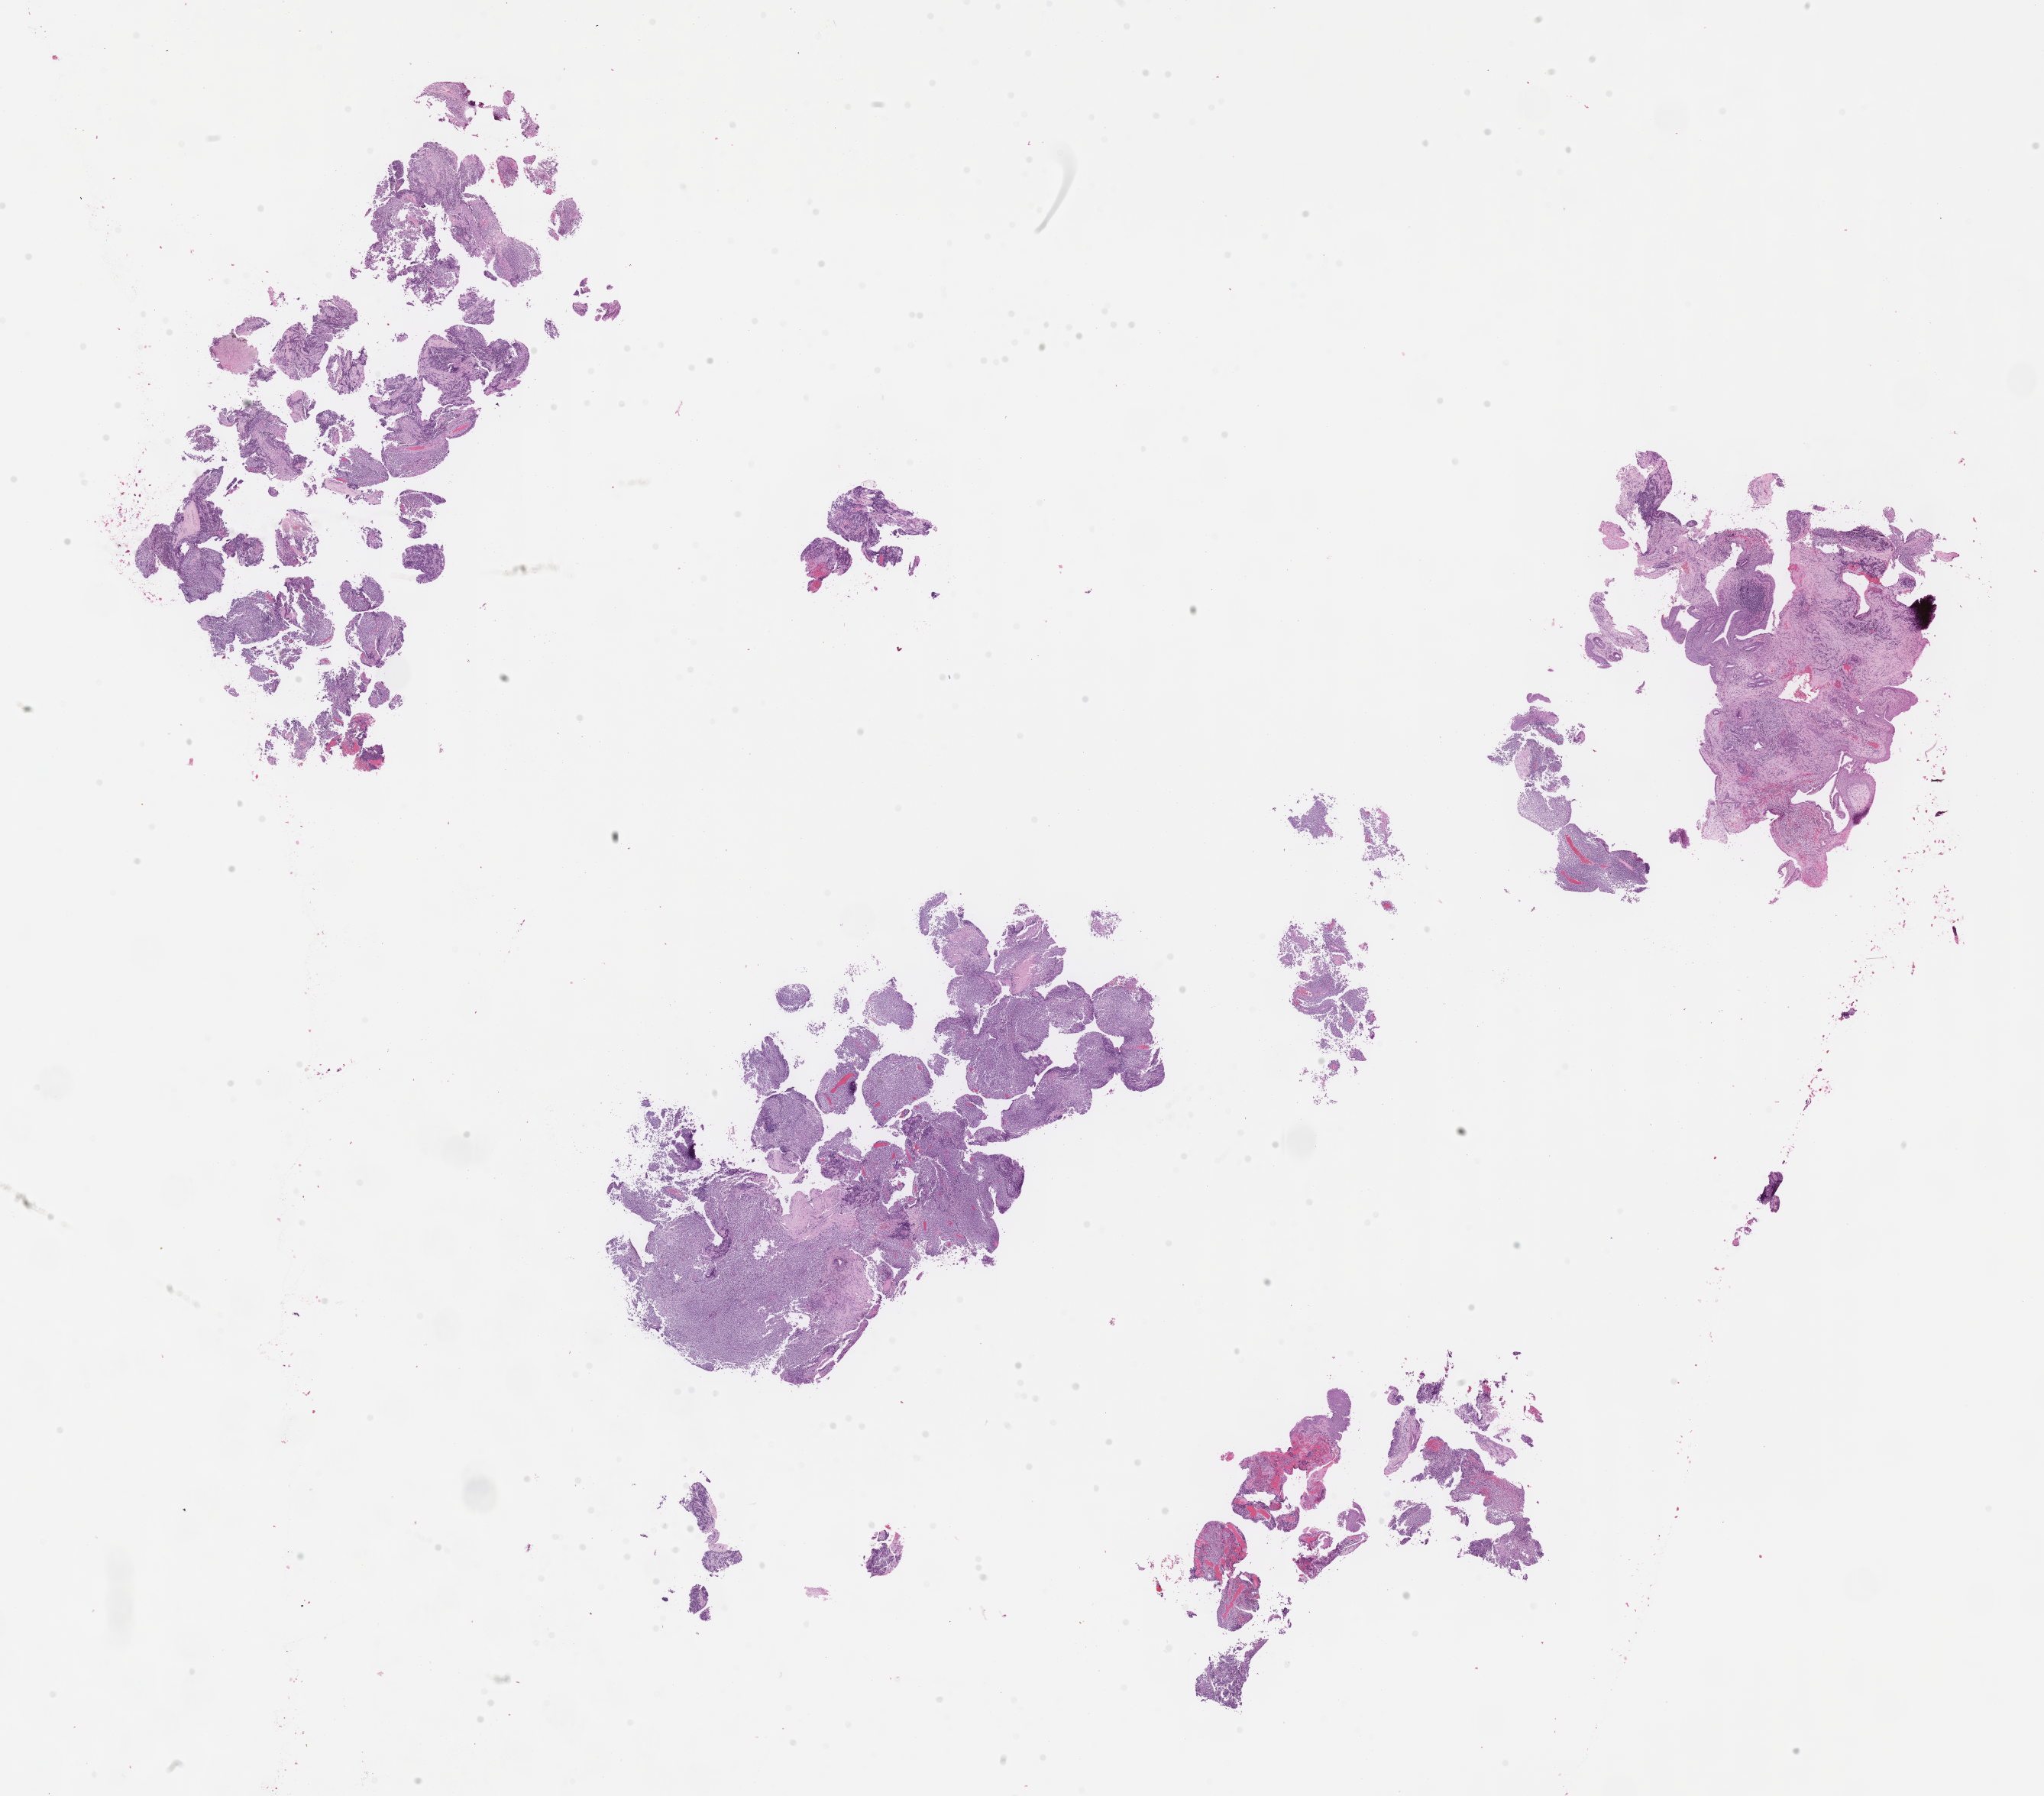
Whole-slide image, hematoxylin and eosin (H&E) stain of tumor tissue — low-resolution overview of the scanned area, about 21.6 x 19.0 mm, FFPE section, sample anatomic site: nasopharynx. Male patient, age at diagnosis 11.4 years.
• metastatic status at presentation (as recorded): non-metastatic
• diagnosis: rhabdomyosarcoma; histological classification: alveolar rhabdomyosarcoma
• stage (as recorded): 3